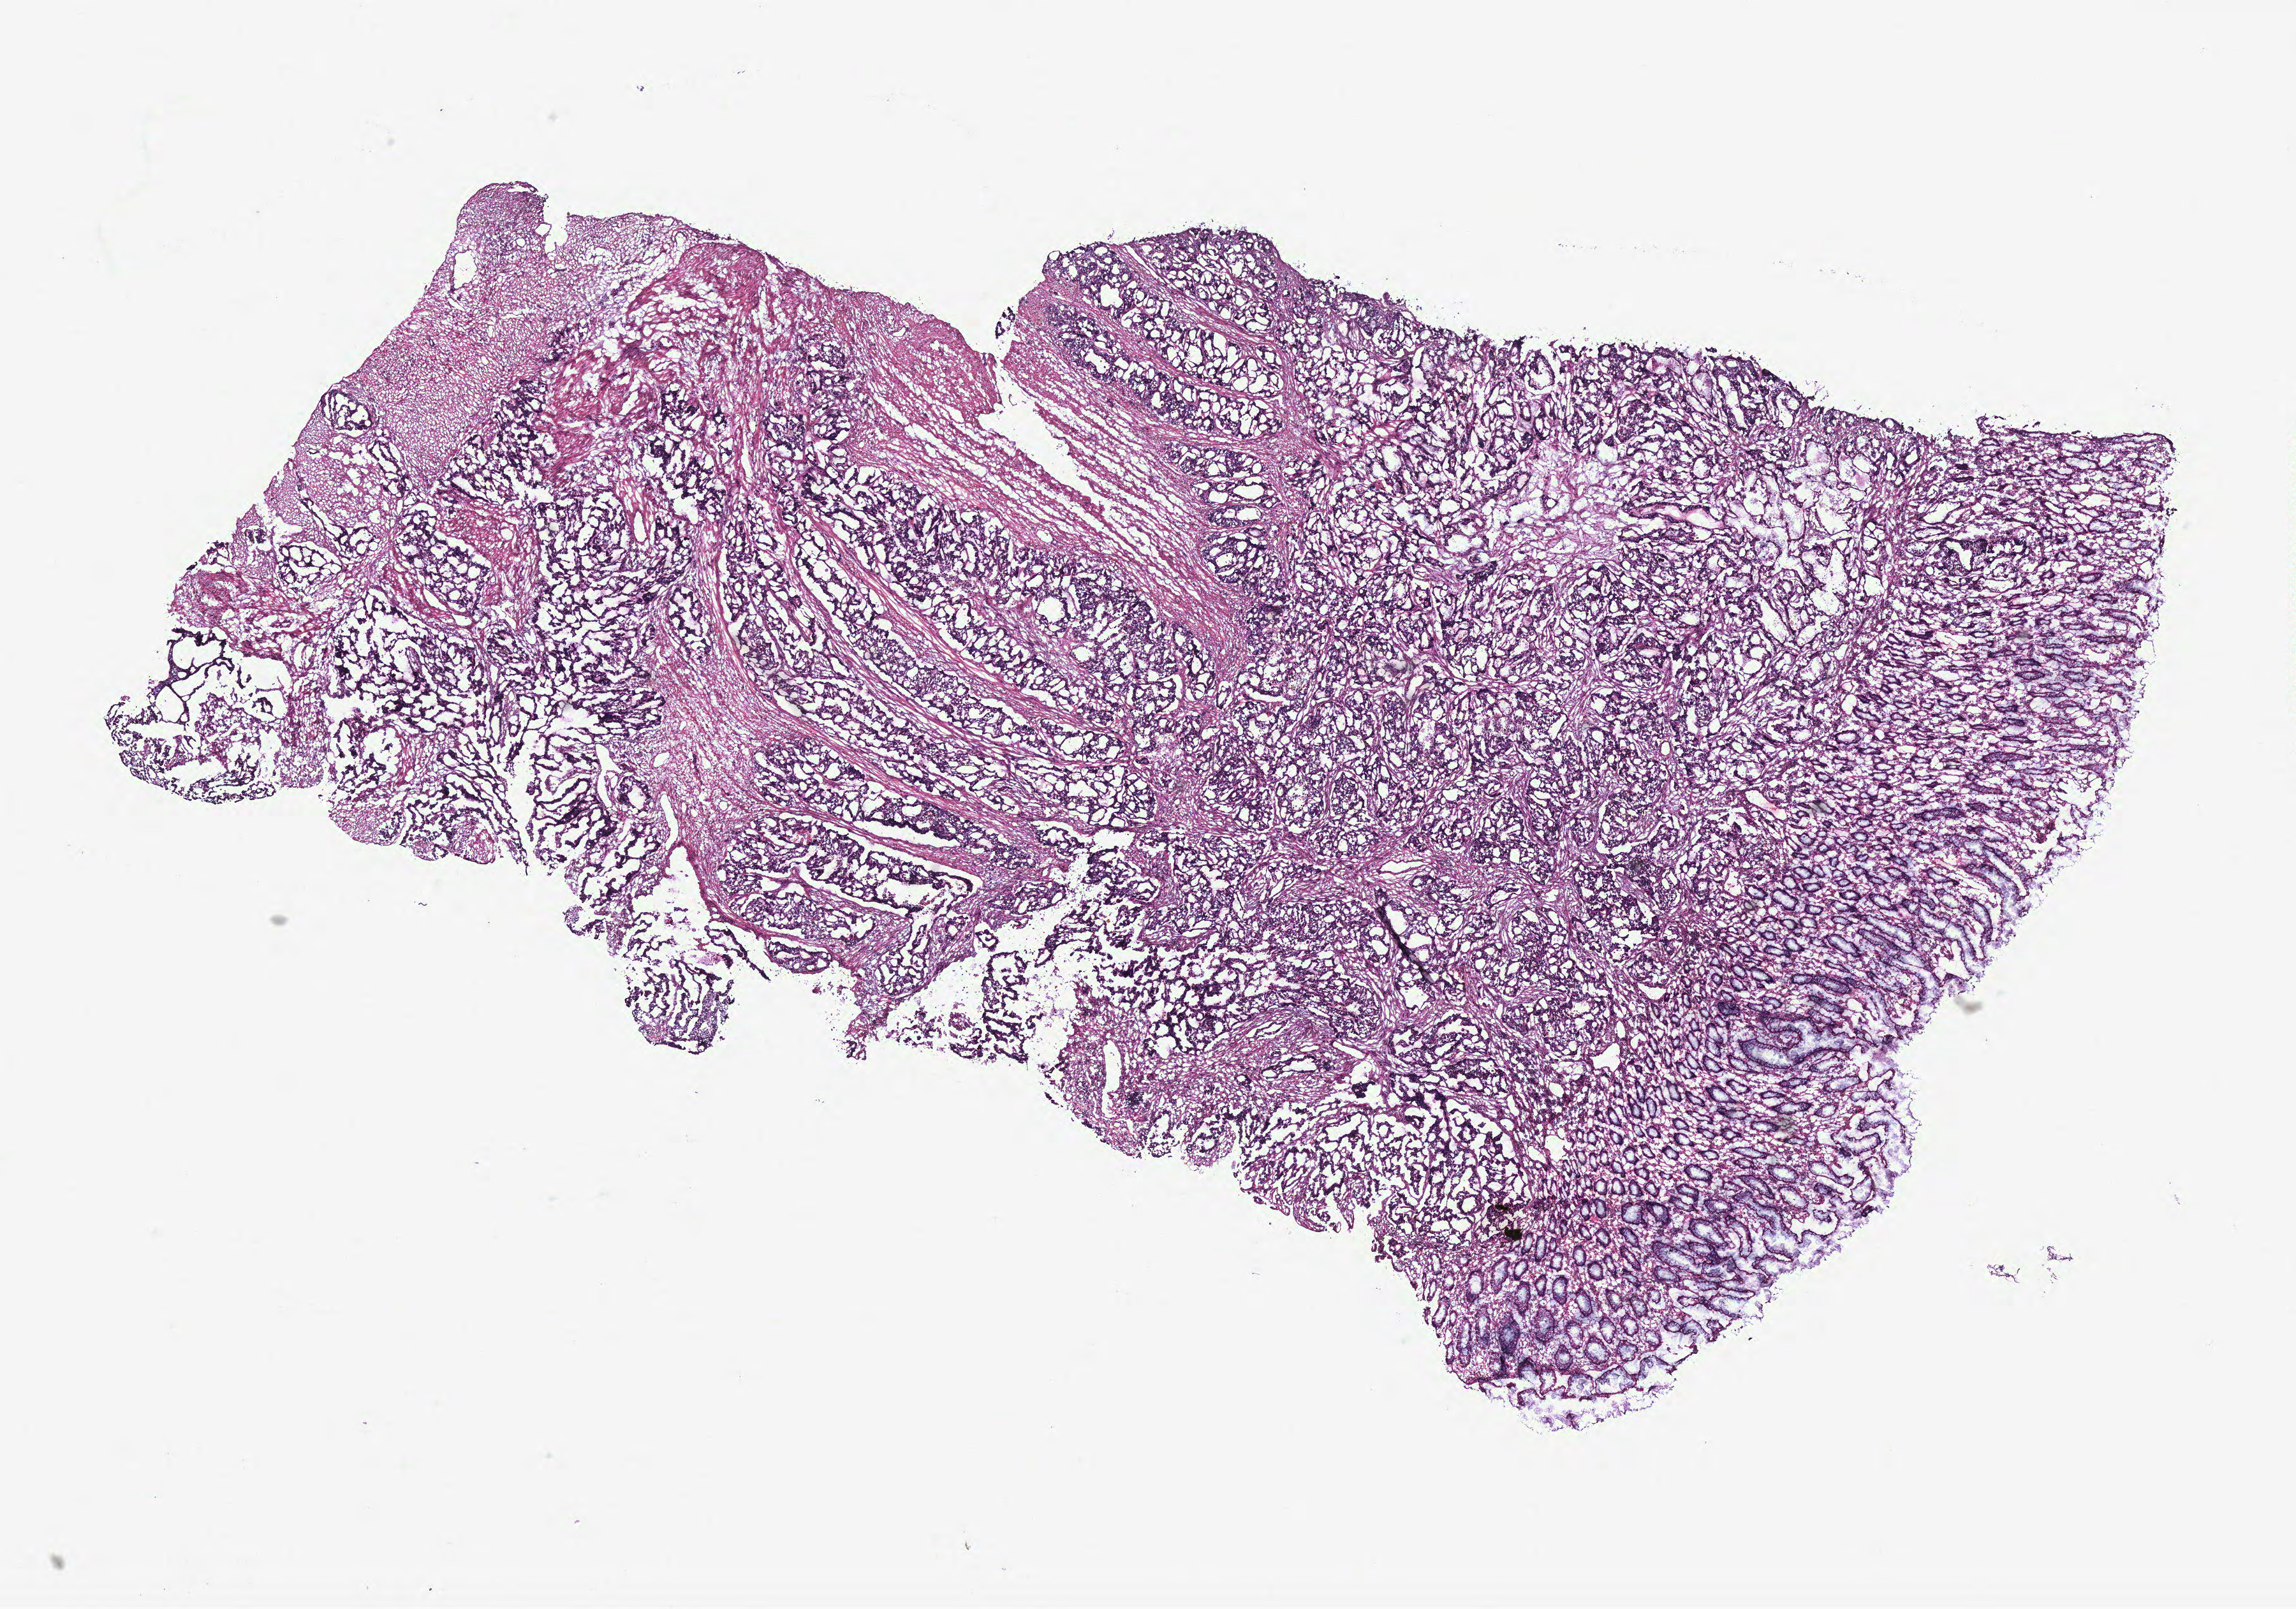
Whole-slide histology image, H&E, low-resolution overview of the scanned area, about 14.4 x 10.1 mm (from a 40x scan), colon, tissue type not recorded.
• patient diagnosis (cohort enrolment): colon cancer (colon)